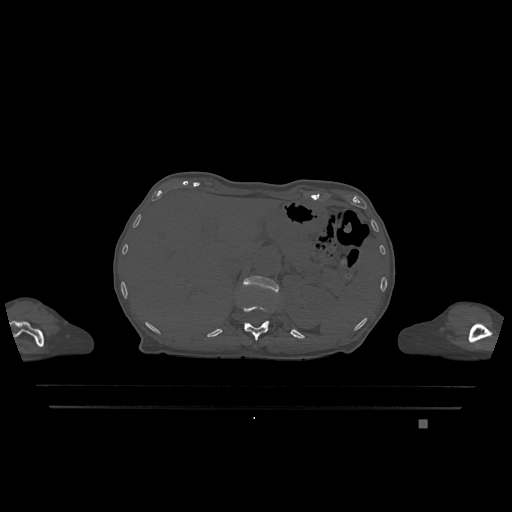
CT including the spine, one axial slice. Position 519 of 1317 along the scan axis. Bone window (W 1800 / L 400 HU). 0.5 mm slice thickness. 512 × 512 image matrix, field of view 500 × 500 mm. Female patient, age 74 years. Case-level facts recorded for this patient, not image findings: primary cancer: lung; vertebrae with lytic lesions (as recorded): T1, T4, T5, T6, L4, L5.
Outlined on this slice (semi-automatically segmented with operator editing):
- L1 vertebra: bounding box [x1, y1, x2, y2] px = [243, 275, 279, 293]
- T12 vertebra: [242, 305, 270, 341]